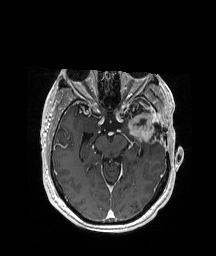
Brain MRI from a brain-tumour surgery series, one axial slice. Slice 123 of 208 in the series (ordered by position). T1-weighted post-contrast. 1 mm slice thickness. 216 × 256 image matrix. Case-level facts recorded for this patient, not image findings: histopathology: Glioblastoma; WHO grade: 4; IDH mutation: no.
Annotated regions visible in this slice (expert manual segmentation):
- previous resection cavity: box from (x=136, y=119) to (x=162, y=134) px
- tumour: (x=123, y=109)–(x=158, y=141)